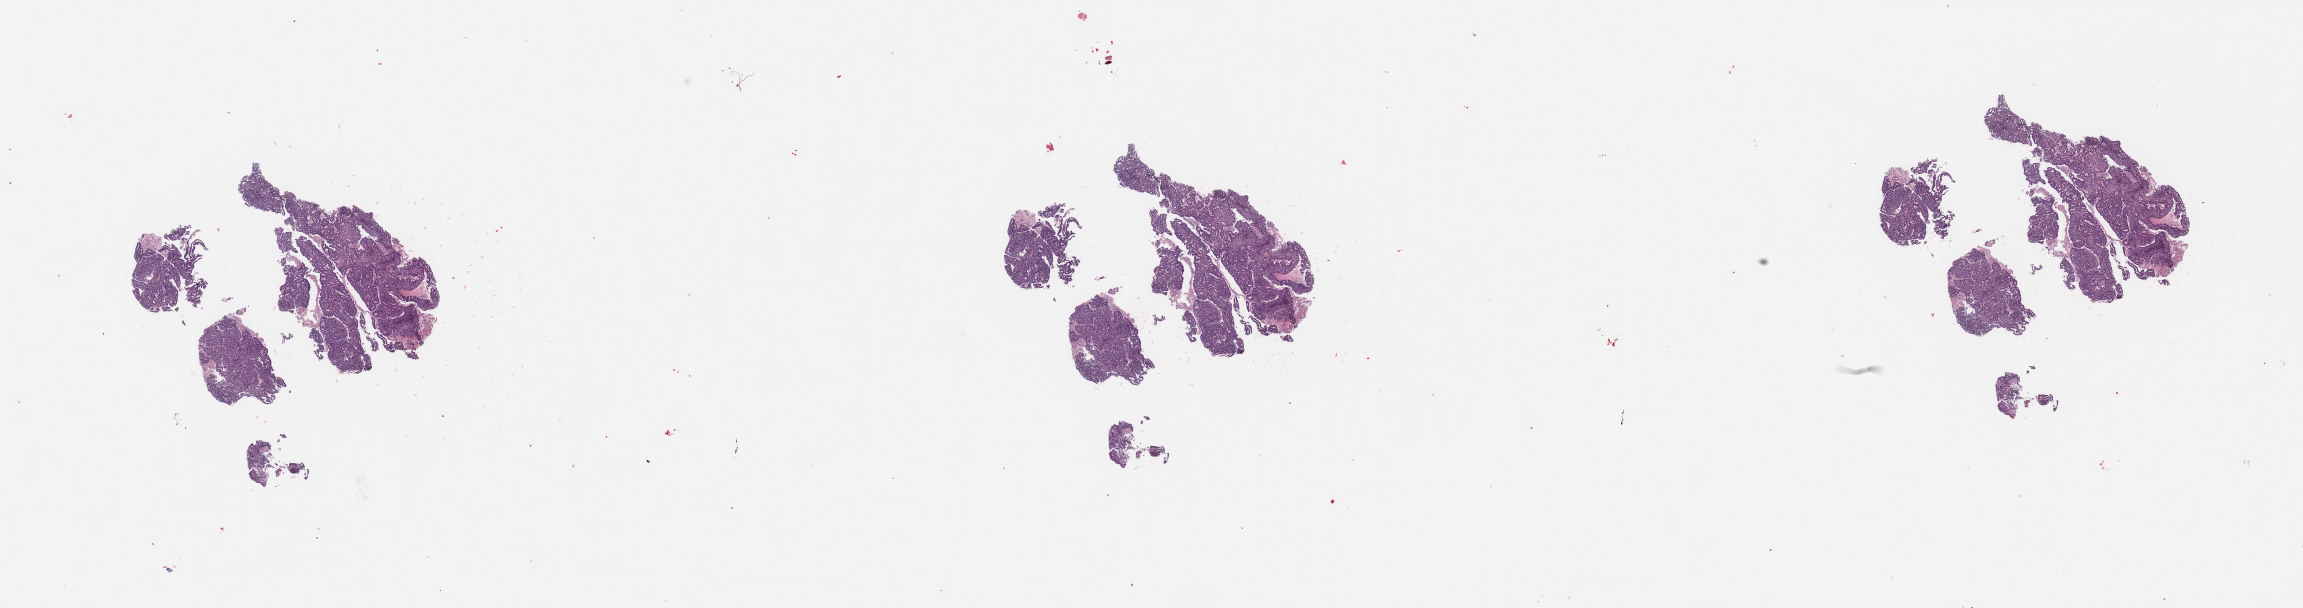
Hematoxylin and eosin (H&E) stained whole-slide image, low-resolution overview of the scanned area, about 36.4 x 9.6 mm. Uterus, tumour tissue. Patient: female, age 53 years. Histologic grade: G2 (moderately differentiated).
Diagnosis: Endometrioid adenocarcinoma, NOS.